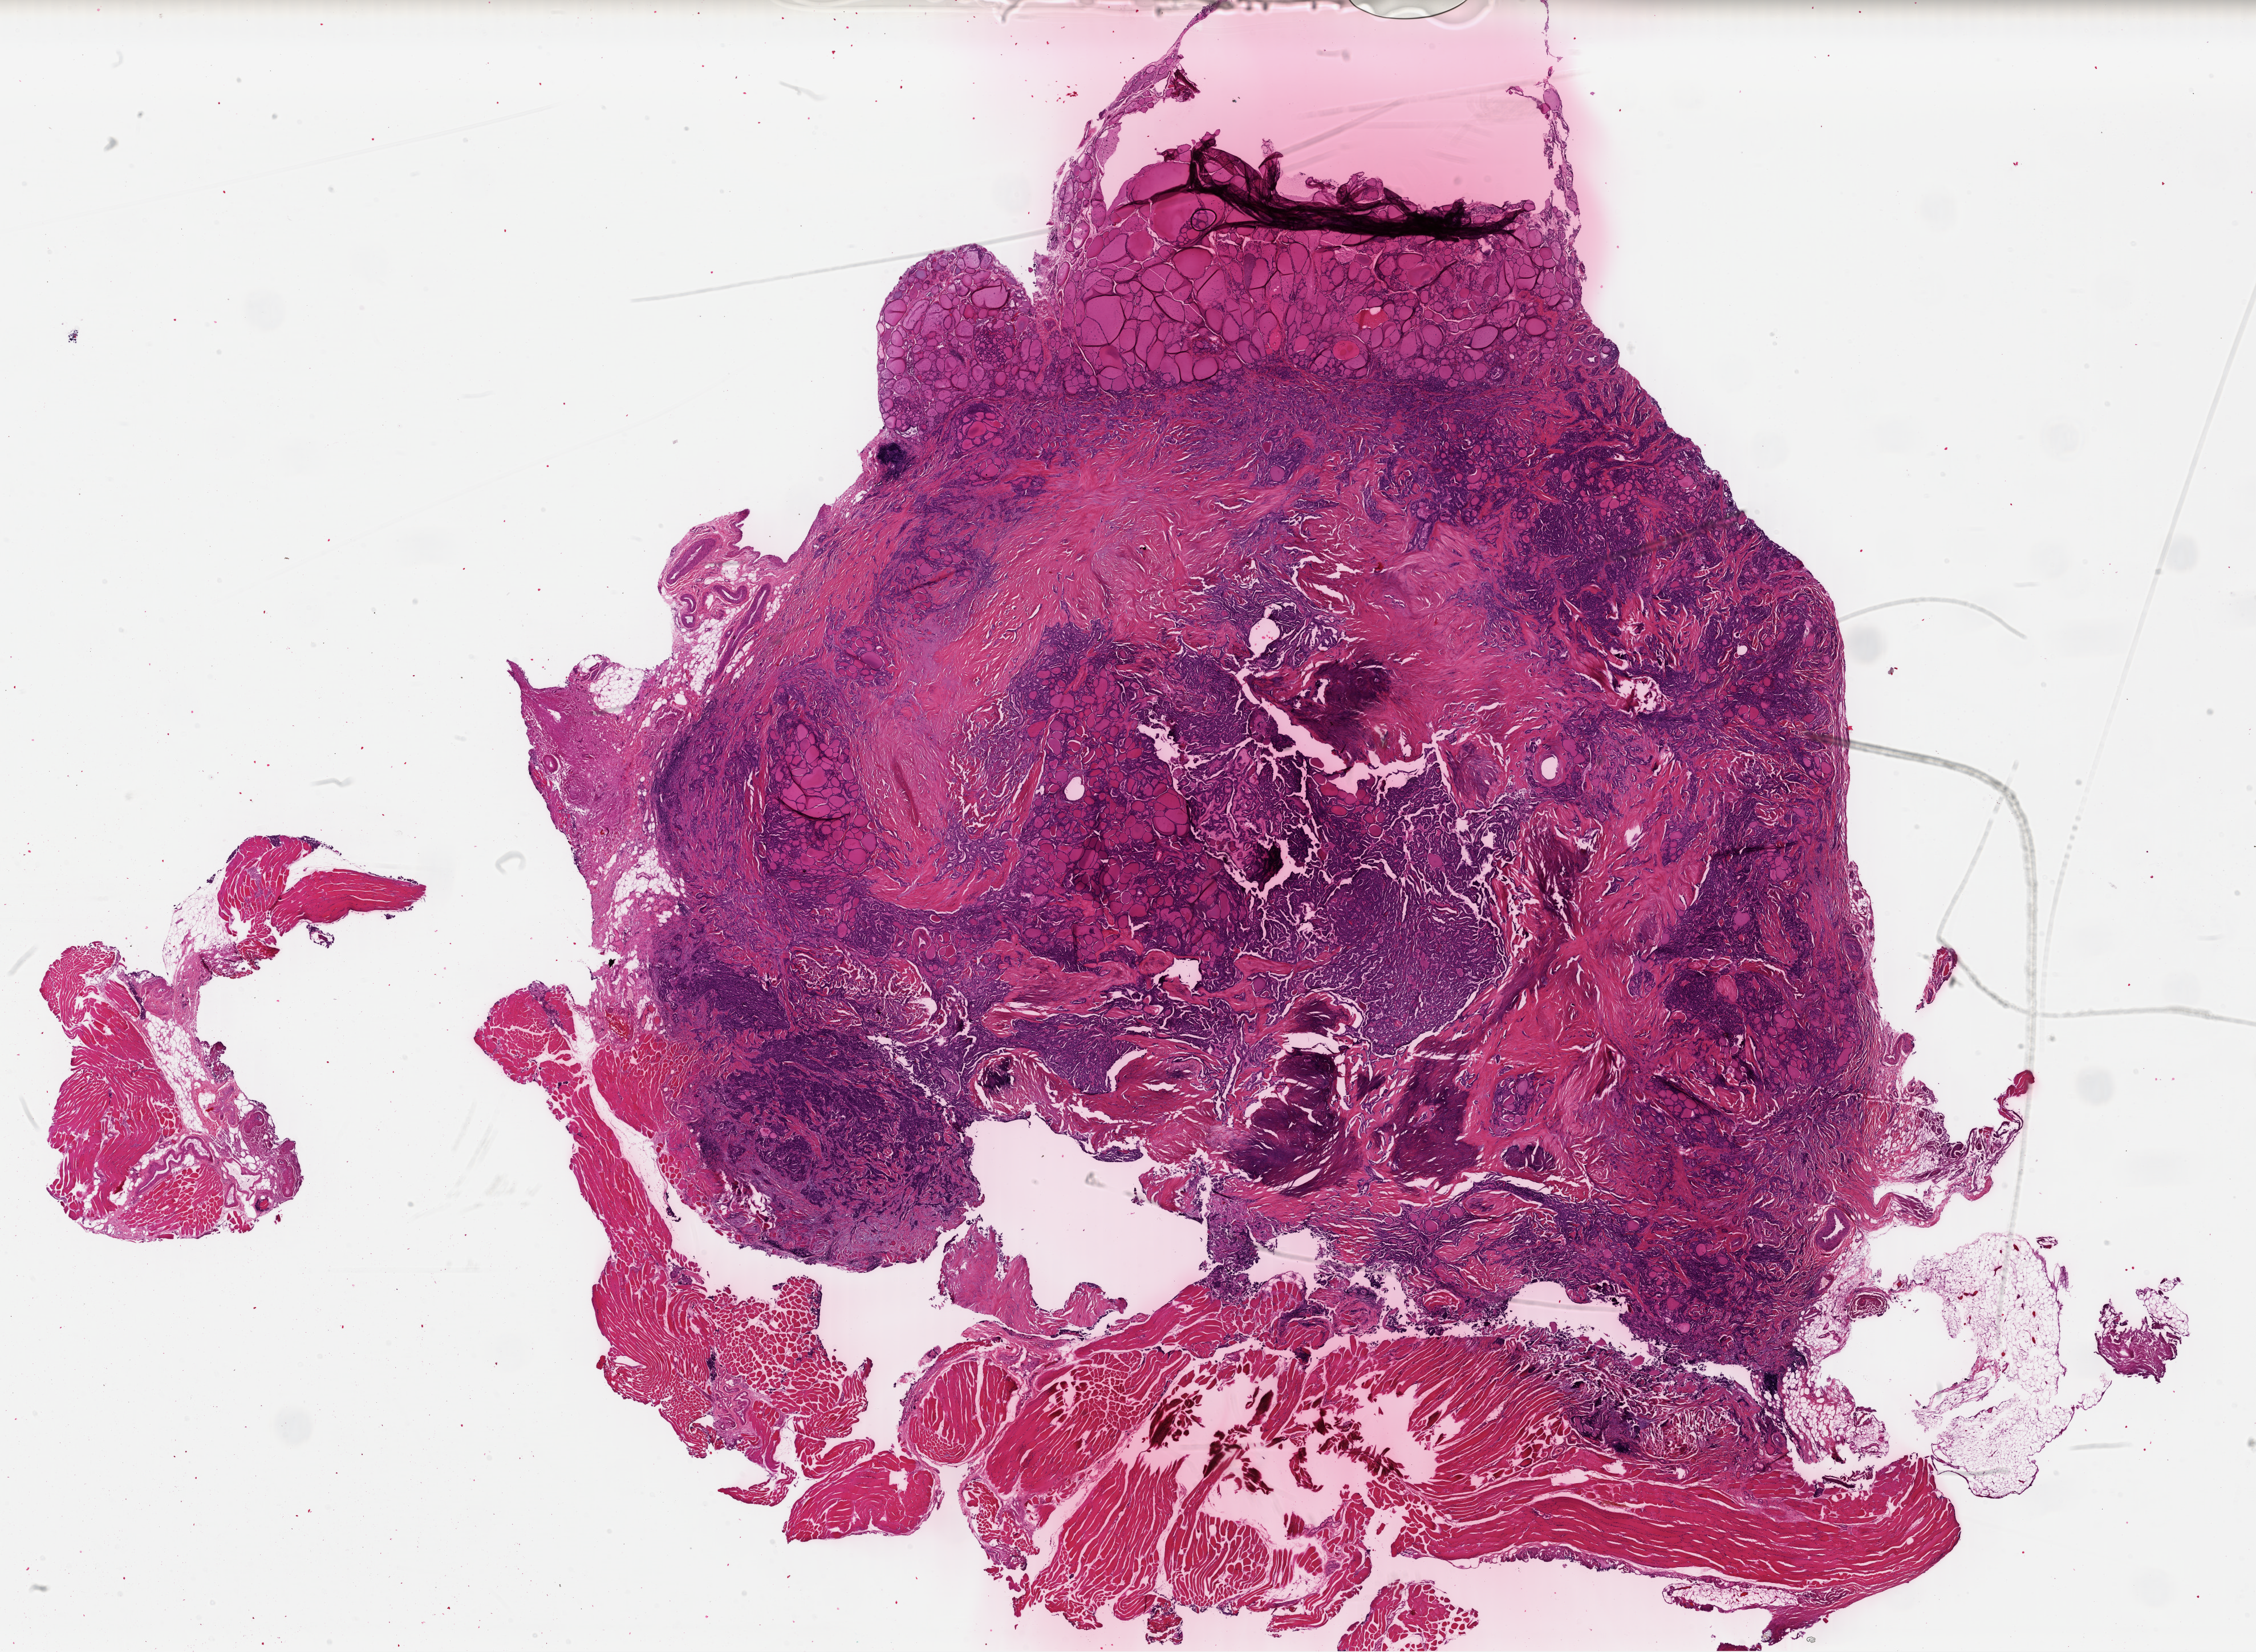
Whole-slide histology image, H&E, shown as a low-resolution overview of the whole scanned area (about 31.1 x 22.8 mm, from a 40x scan). Formalin-fixed paraffin-embedded (FFPE) diagnostic section. Primary tumour sample from the thyroid. Patient: female, age at initial diagnosis 68 years.
Histologic diagnosis: Papillary adenocarcinoma, NOS (thyroid gland).